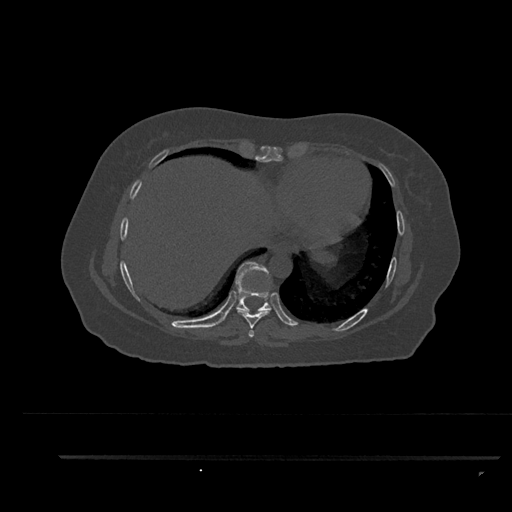
CT including the spine, one axial slice. Position 440 of 797 along the scan axis. Reconstruction kernel Br40s/3. 120 kVp. Bone window (W 1800 / L 400 HU). 0.5 mm slice thickness. 512 × 512 image matrix, field of view 408 × 408 mm. Female patient, age 44 years. Case-level facts recorded for this patient, not image findings: primary cancer: renal; vertebrae with lytic lesions (as recorded): L1.
Outlined on this slice (semi-automatically segmented with operator editing):
- T7 vertebra: box from (x=248, y=330) to (x=255, y=338) px
- T8 vertebra: (x=237, y=310)–(x=271, y=329)
- T9 vertebra: (x=235, y=262)–(x=272, y=312)